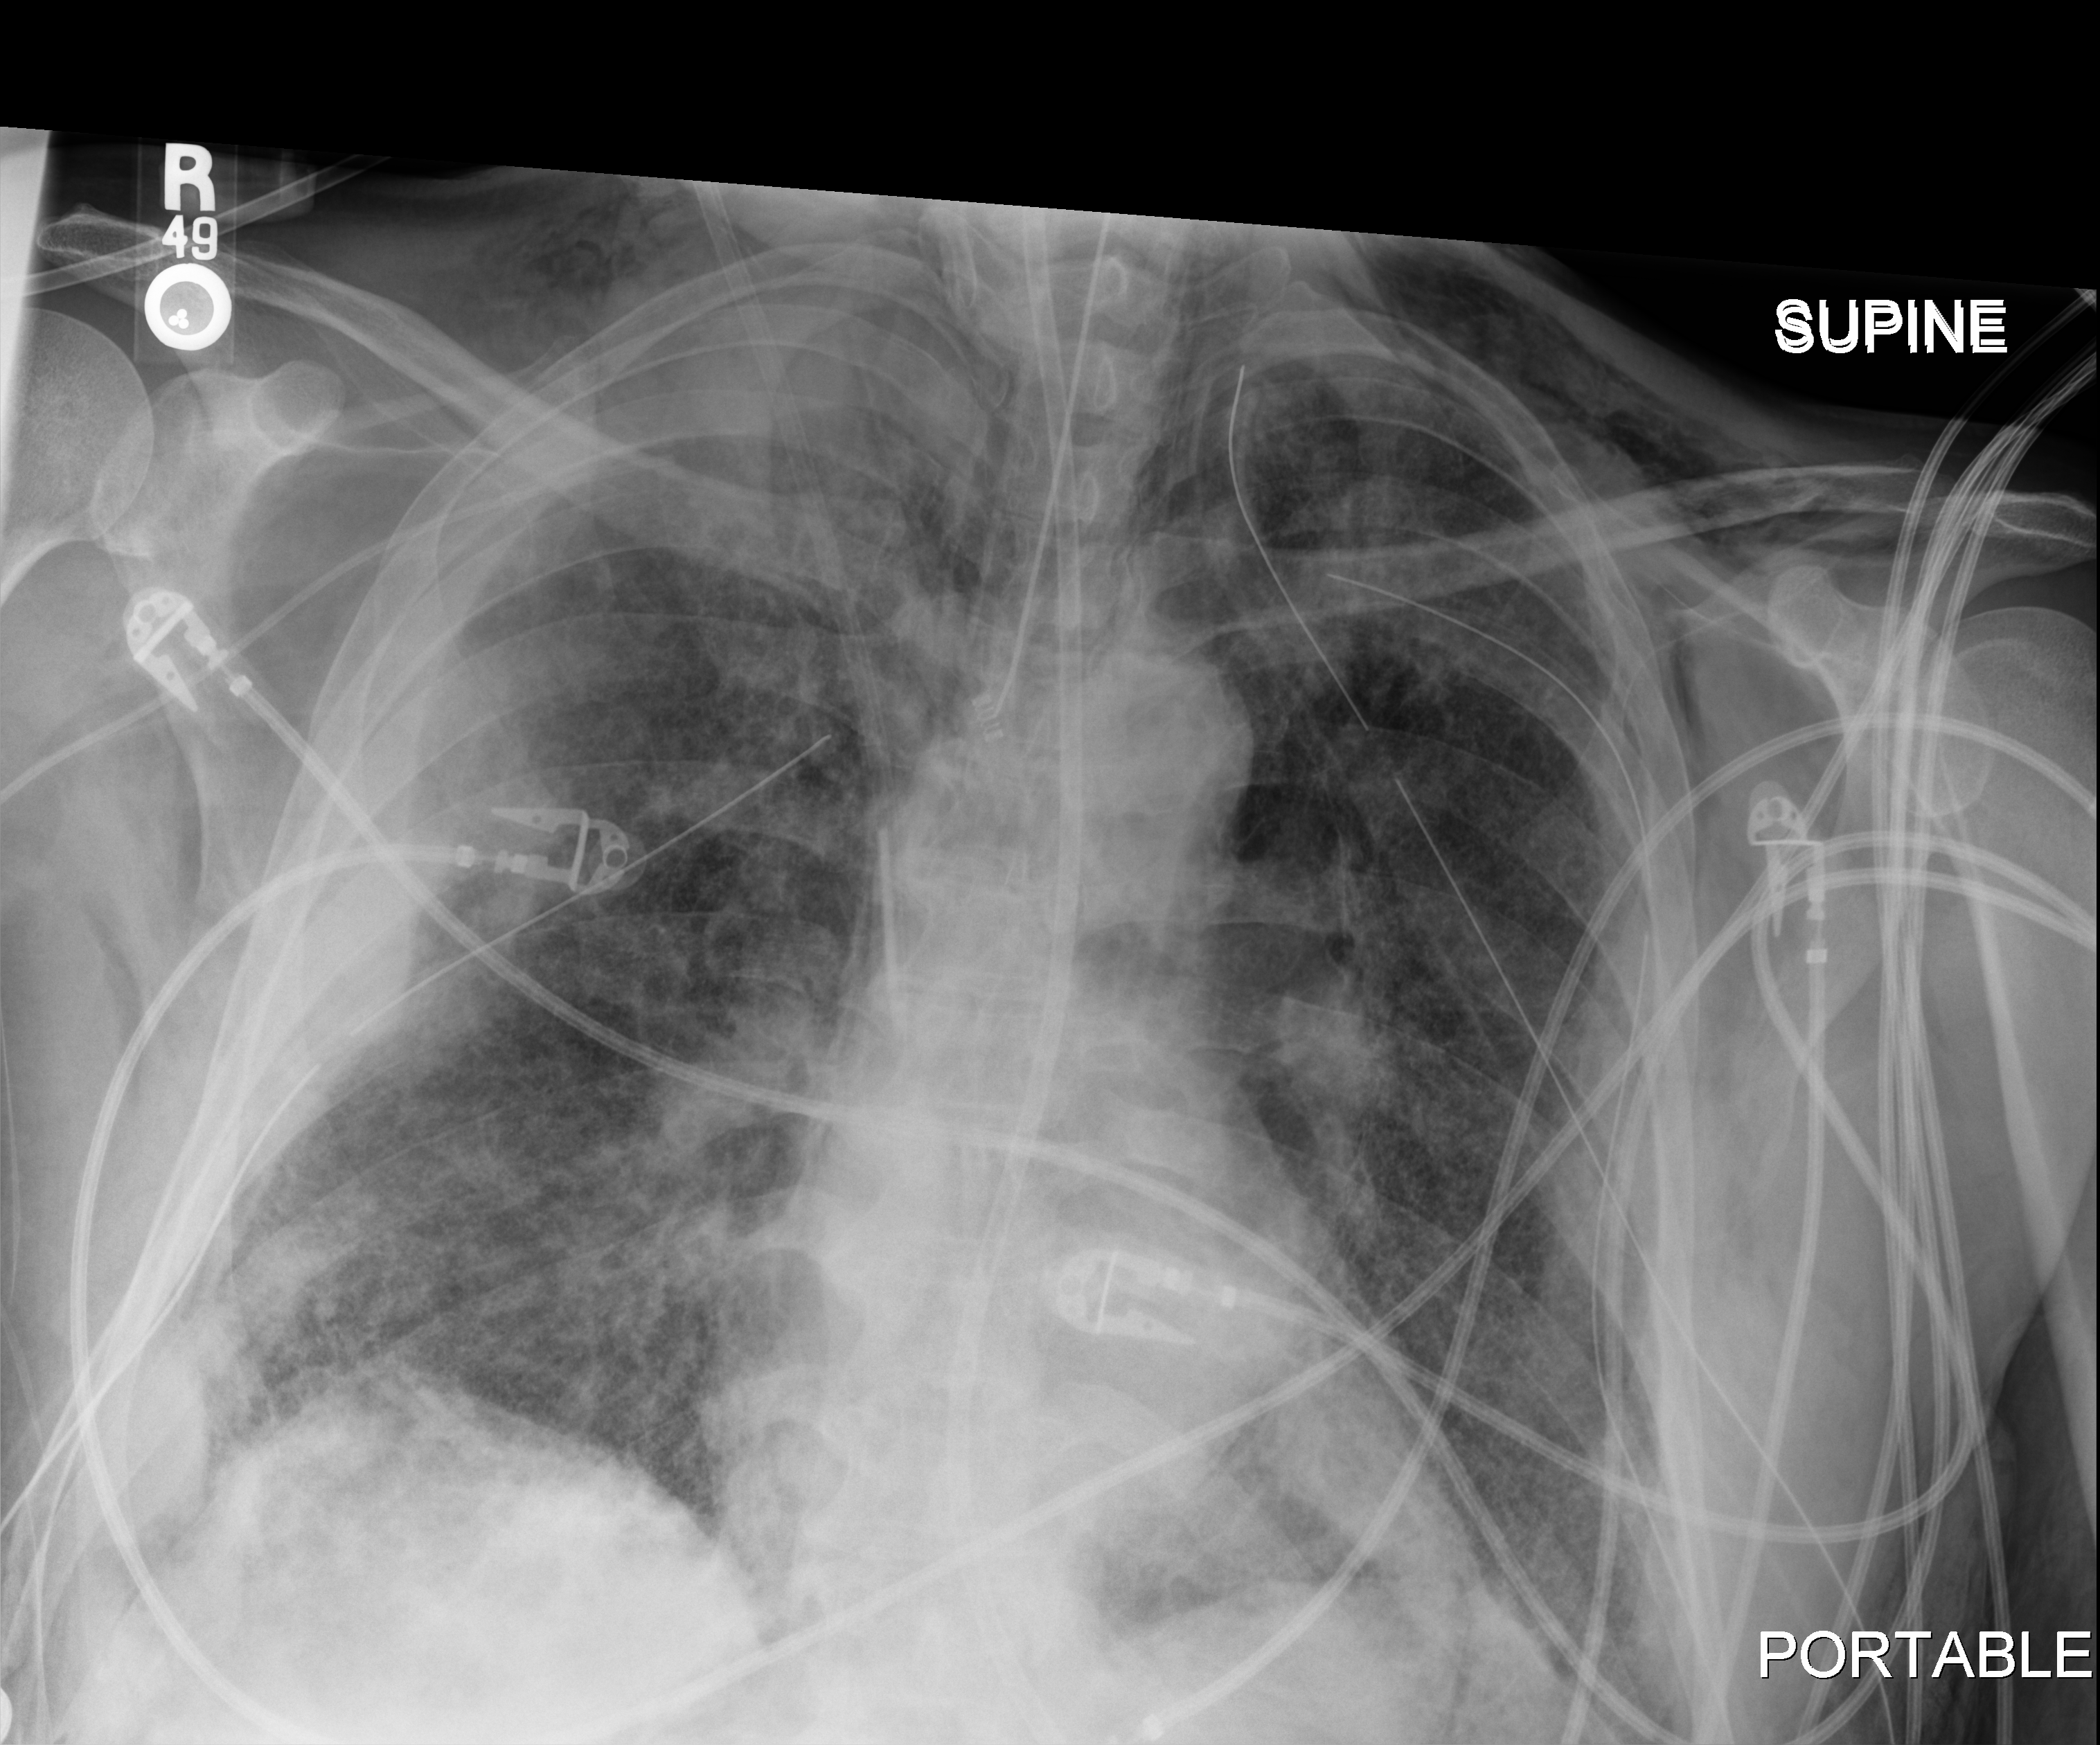
Bedside chest radiograph (digital radiography); anteroposterior (AP) projection. Male patient hospitalised with COVID-19, age 18–59 years.
From the hospital-stay record, not from the radiograph (when in the stay this image was taken is not recorded):
- length of hospital stay: 42 days